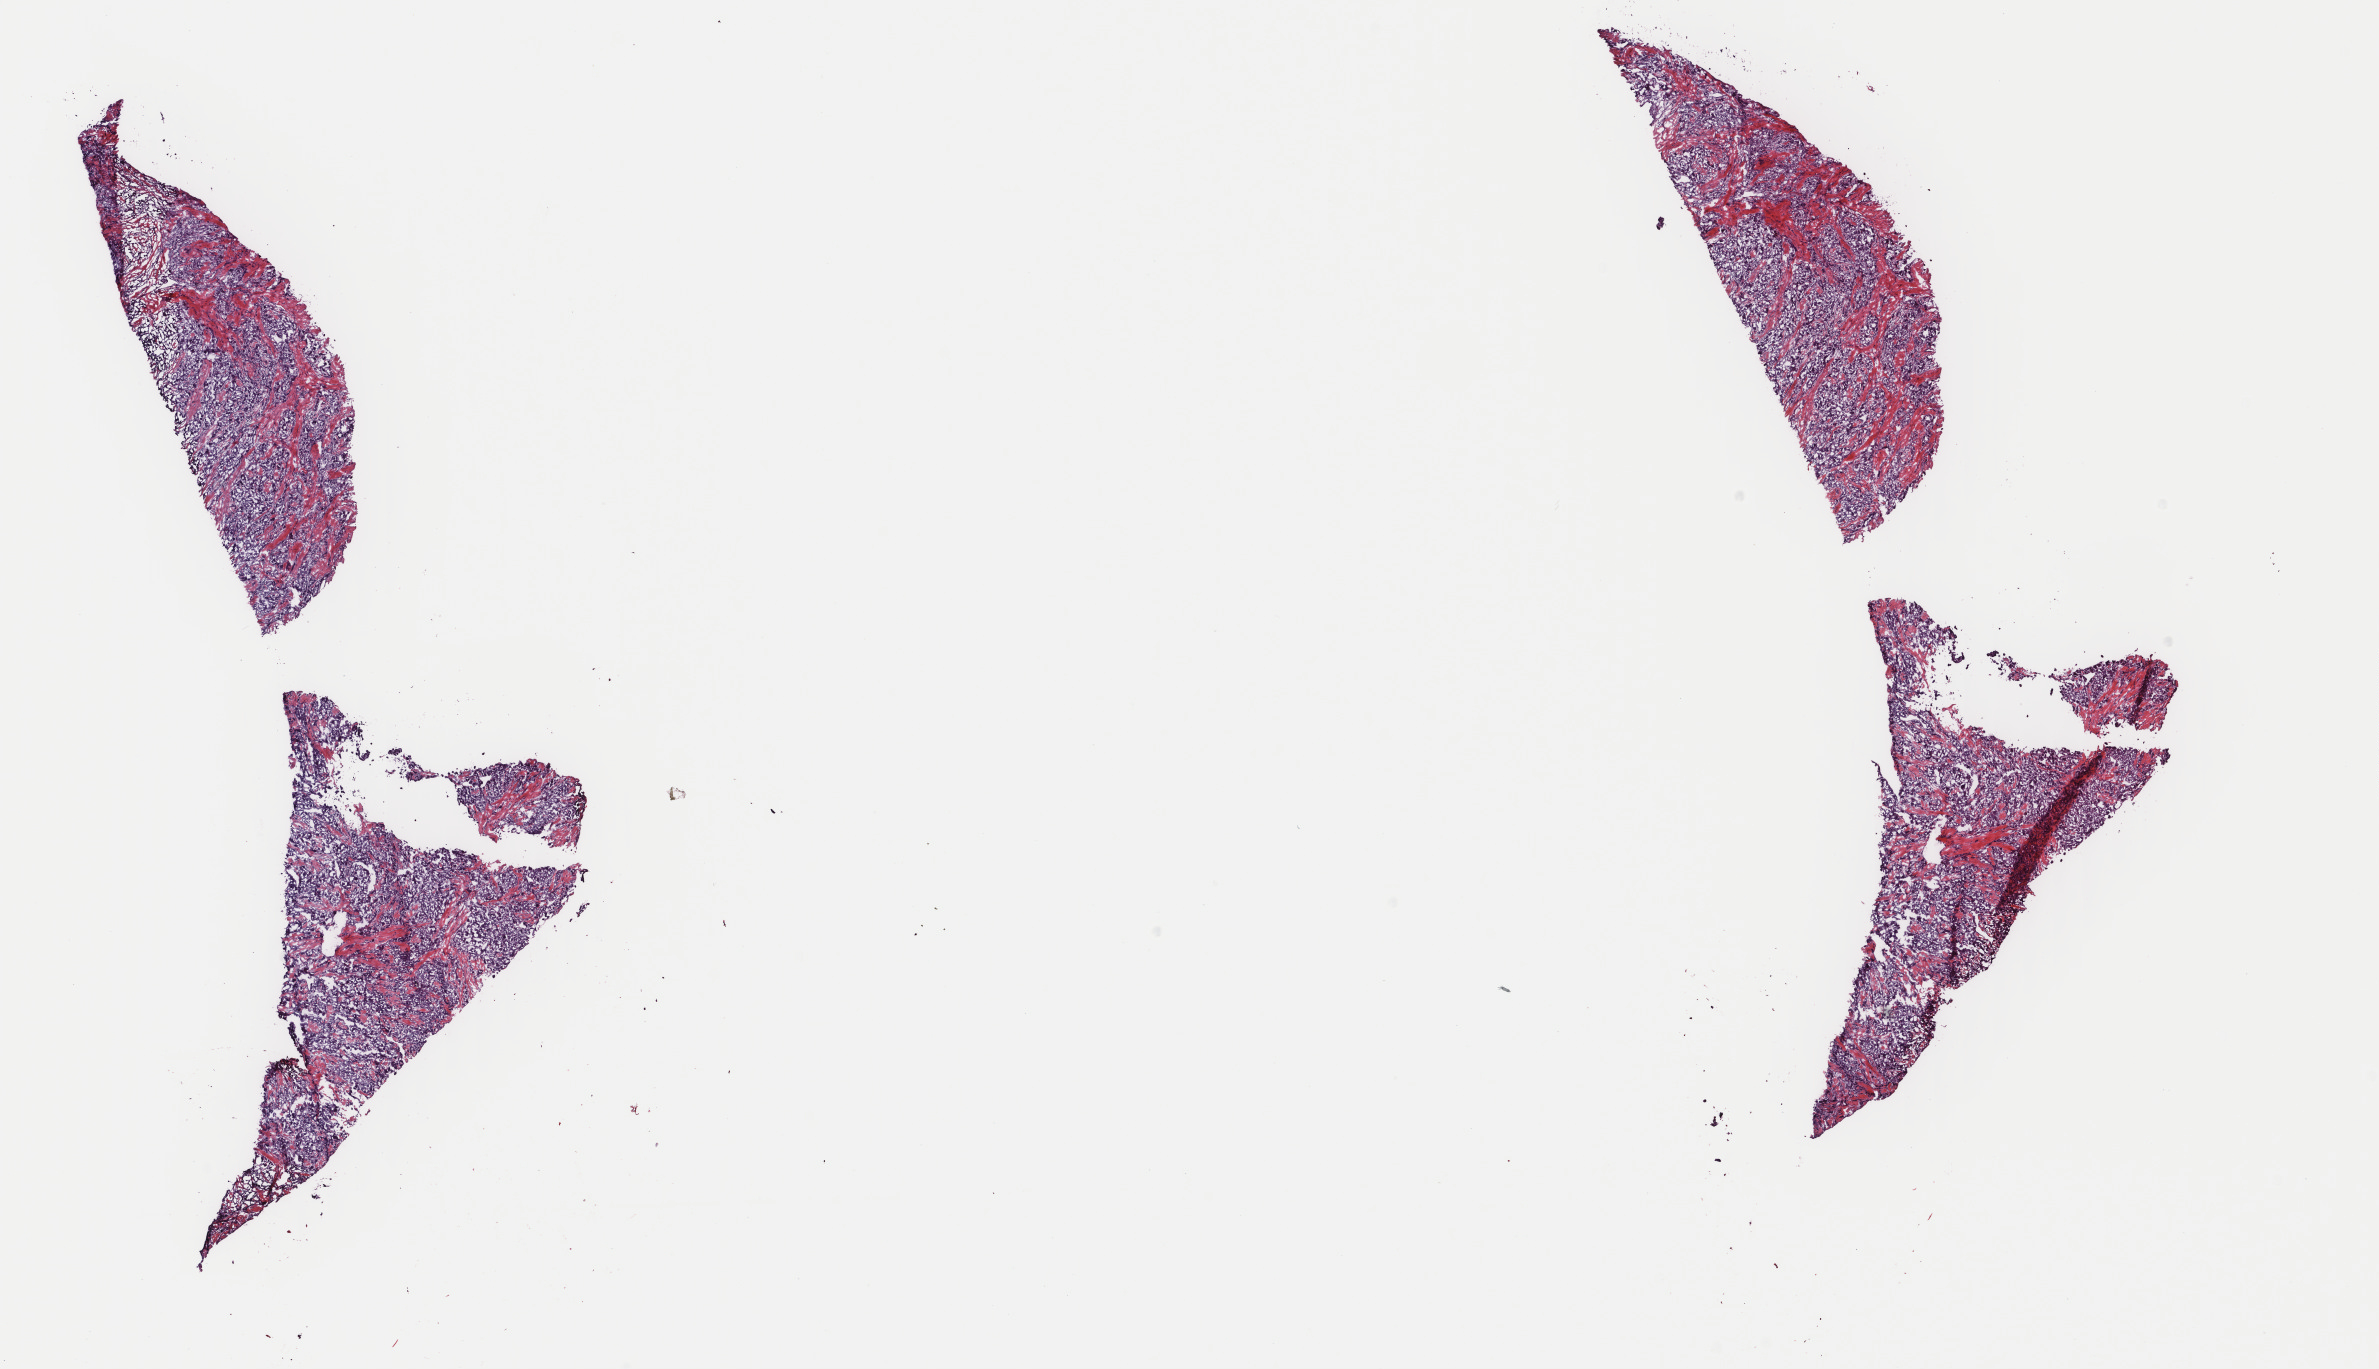
Hematoxylin and eosin (H&E) stained whole-slide image, whole scanned area (about 18.9 x 10.9 mm, slide scanned at 40x) shown as a low-resolution overview; frozen section from the top of the tissue portion; liver, primary tumour sample. Patient: female, age at initial diagnosis 20 years. Histologic grade: G2 (moderately differentiated). Composition of this section per pathologist review: tumour cells 69%, tumour nuclei 90%, normal cells 0%, stromal cells 30%, necrosis 1%. Infiltration values recorded for this section: lymphocyte infiltration 4%, monocyte infiltration 0%, neutrophil infiltration 0%.
AJCC pathologic stage: IVA (7th edition). Diagnosis: Hepatocellular carcinoma, fibrolamellar.